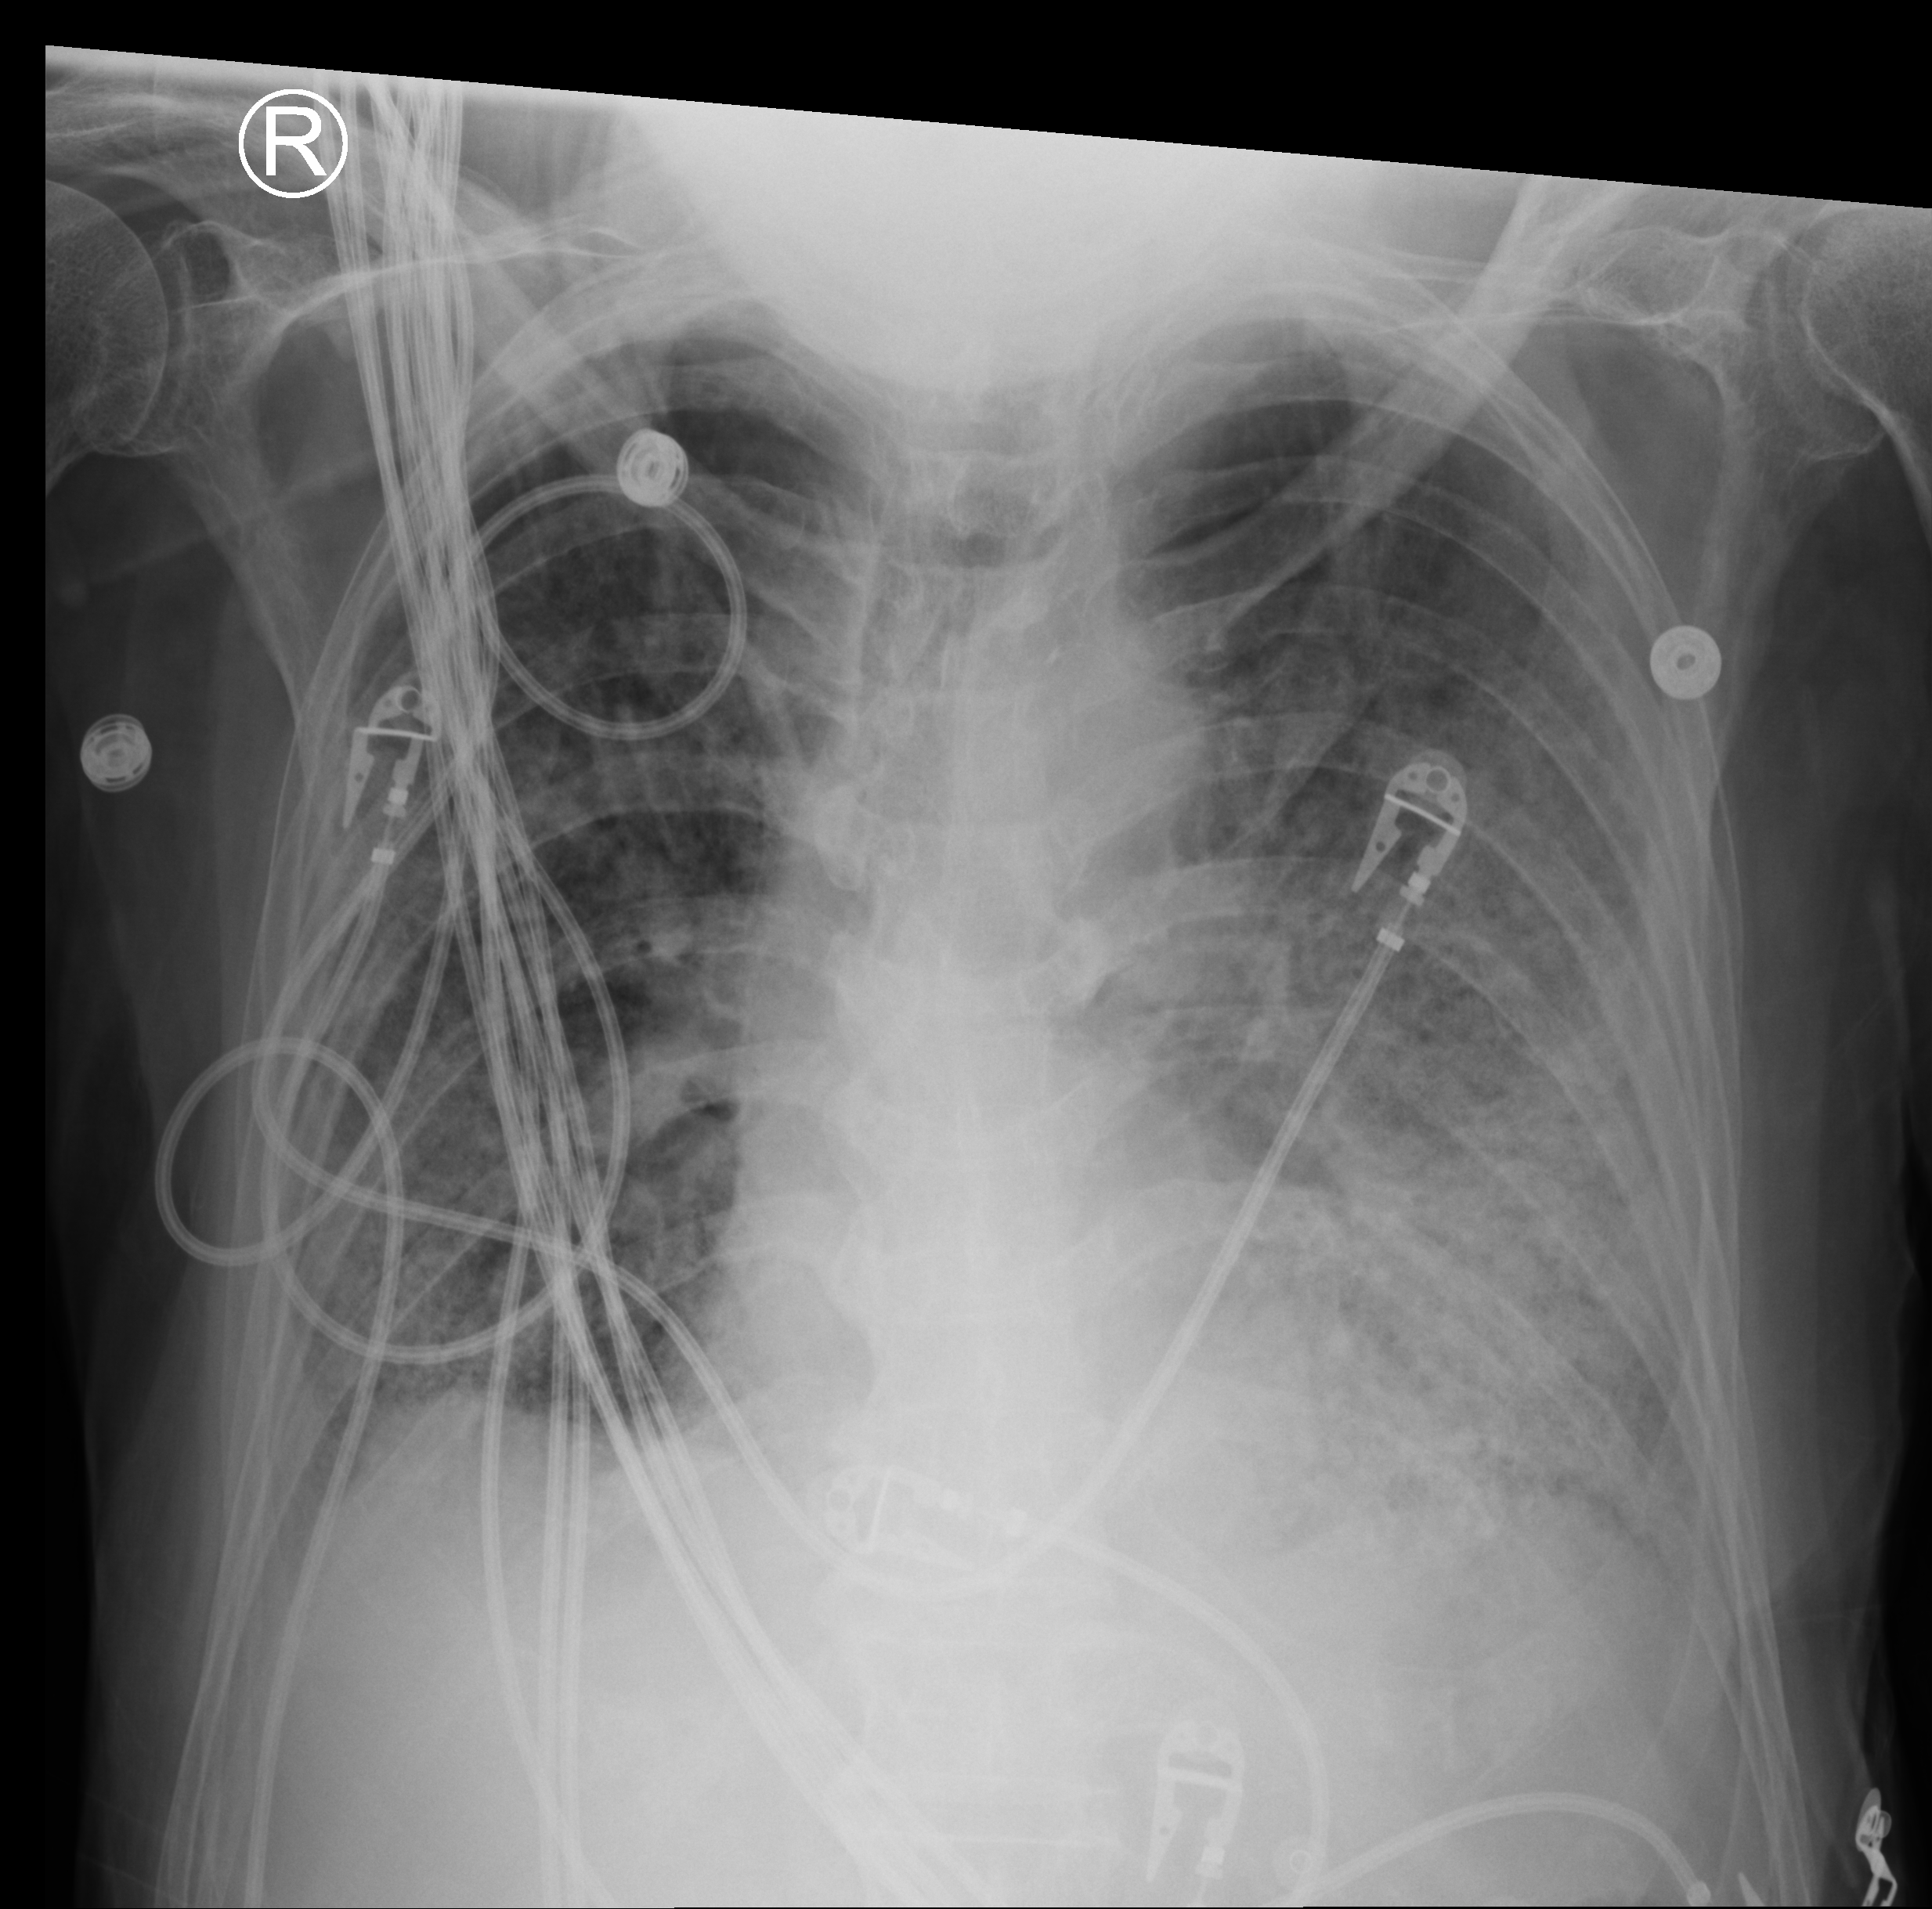
Portable chest radiograph; anteroposterior (AP) projection. Male patient hospitalised with COVID-19, age 60–74 years.
Admission-level facts for this patient (not findings on this image; timing relative to this image not recorded): diabetes (admission record): yes; admitted to intensive care during this hospital stay: yes; mechanically ventilated during this hospital stay: yes.